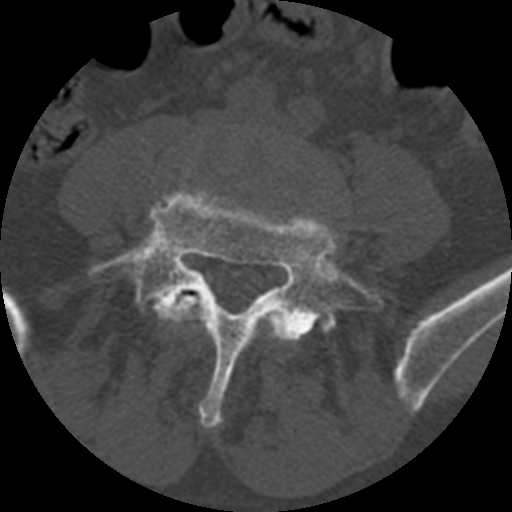
CT including the spine, one axial slice; position 262 of 399 along the scan axis; reconstruction kernel STANDARD; 120 kVp; bone window (W 1800 / L 400 HU); 1.25 mm slice thickness; 512 × 512 image matrix. Patient age 71 years. From the clinical record (not read from this slice): primary cancer: prostate.
Structures marked on this image (semi-automatically segmented with operator editing):
- L4 vertebra: box from (x=170, y=294) to (x=290, y=343) px
- L5 vertebra: (x=87, y=187)–(x=384, y=428)